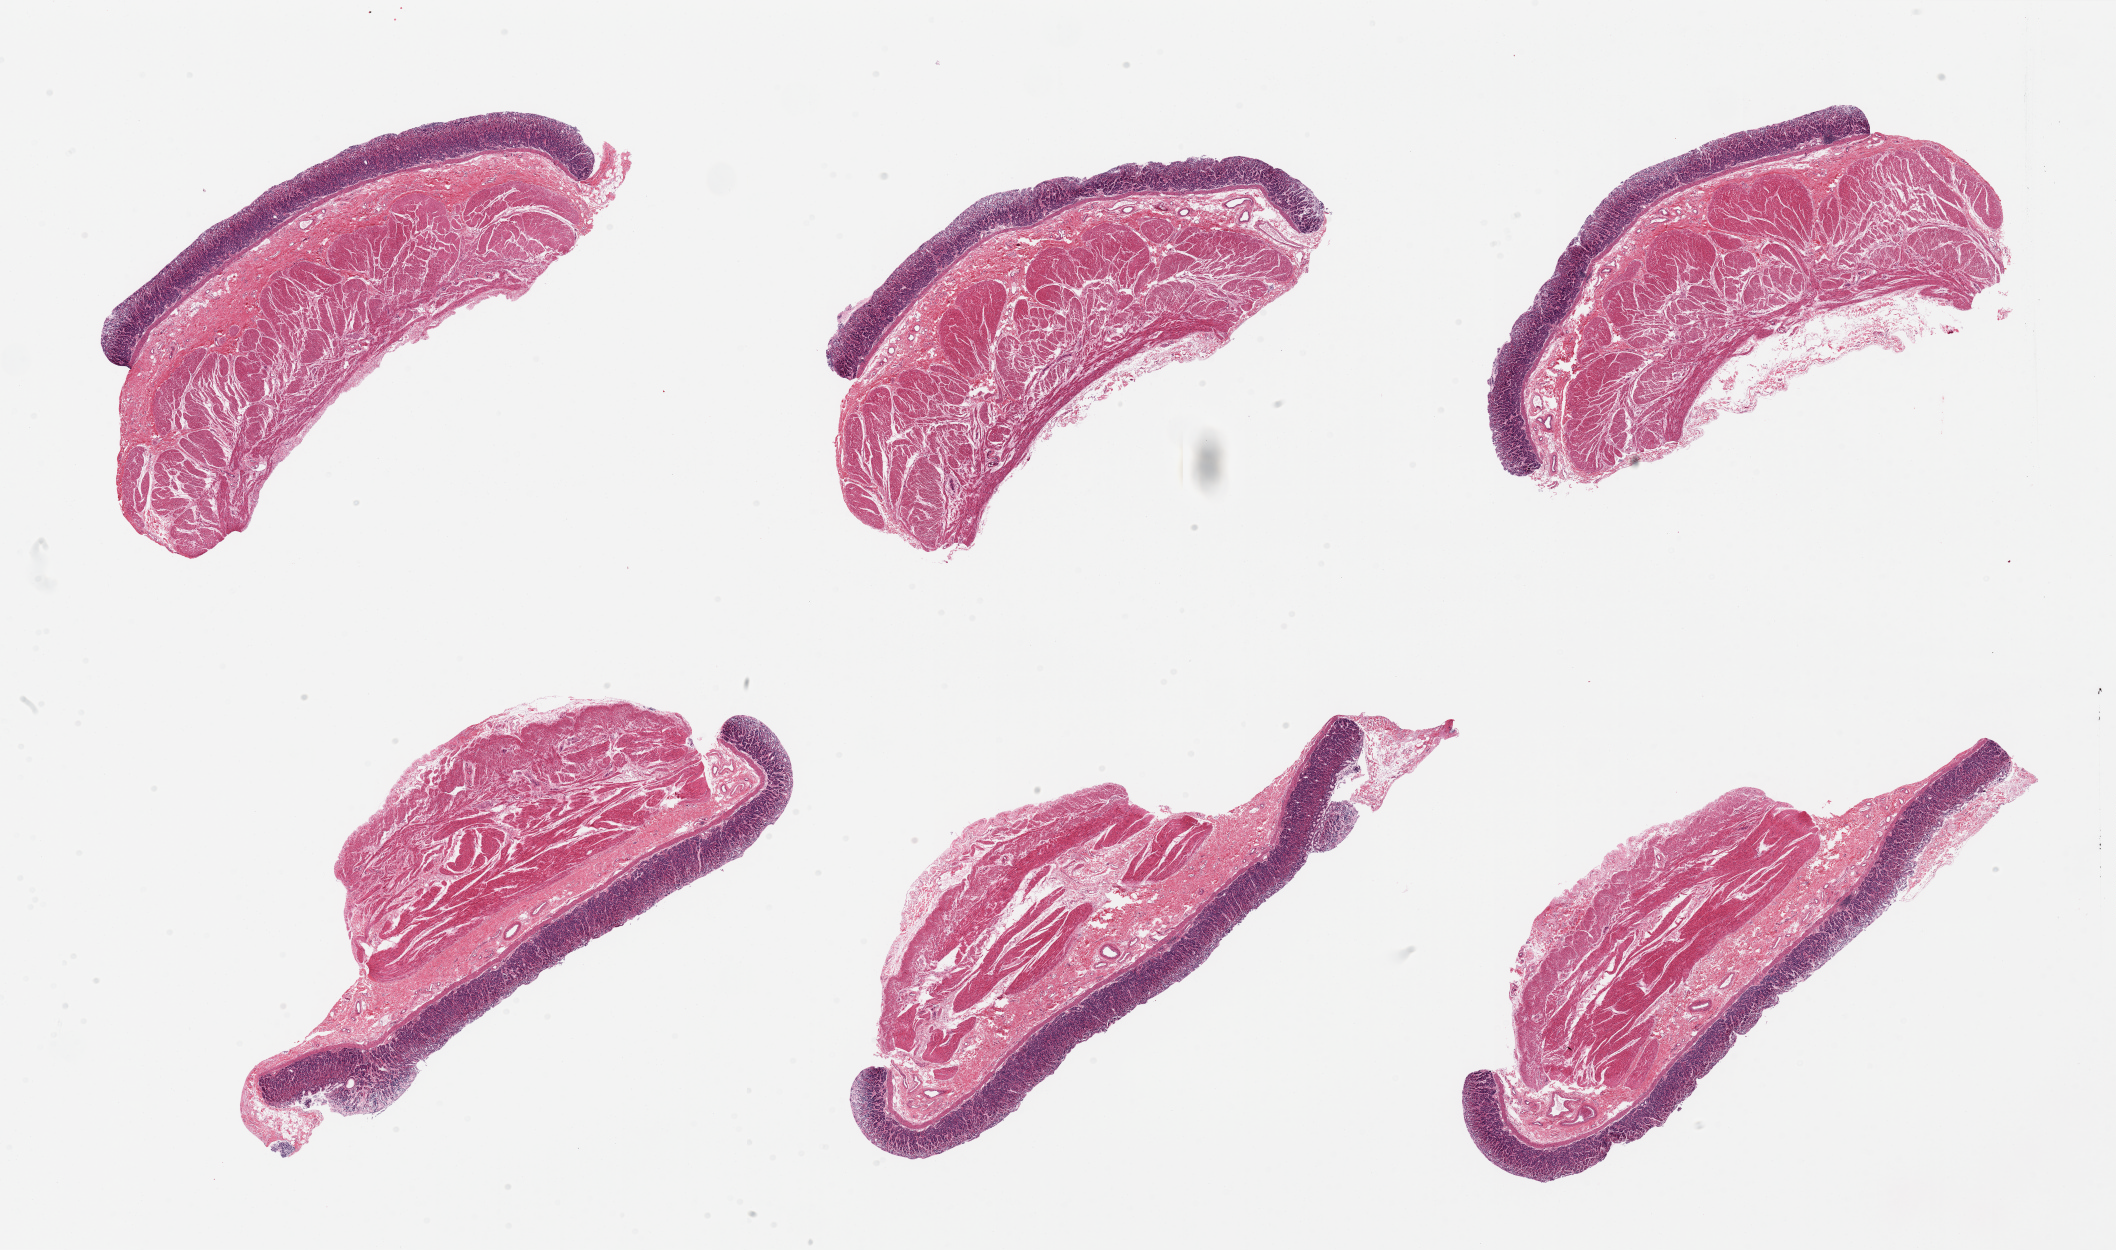
Whole-slide image, H&E stain, brightfield, low-resolution overview of the scanned area, about 33.5 x 19.8 mm. PAXgene-fixed paraffin-embedded (PFPE) section. Section of stomach (target tissue). Donor tissue sample. Donor: female.
Pathologist's review note for this sample: 6 pieces, fairly well preserved mucosa, ~10-15% thickness, superficial areas approach 'score 2' focally.